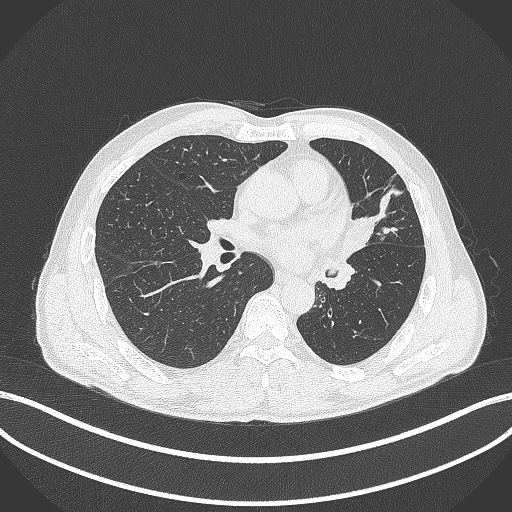
Chest CT, one axial slice. Position 219 of 429 along the scan axis. Reconstruction kernel B70f. Lung window (W 1500 / L -600 HU). 1 mm slice thickness. 512 × 512 image matrix, field of view 400 × 400 mm. Patient: male, 57 years. Case-level facts recorded for this patient, not image findings: clinical TNM (as recorded): T2b N0 M0.
Structures marked on this image (rectangle marked by the reading radiologist):
- lung tumour (recorded histology: squamous cell carcinoma): bounding box [x1, y1, x2, y2] px = [339, 214, 372, 262]